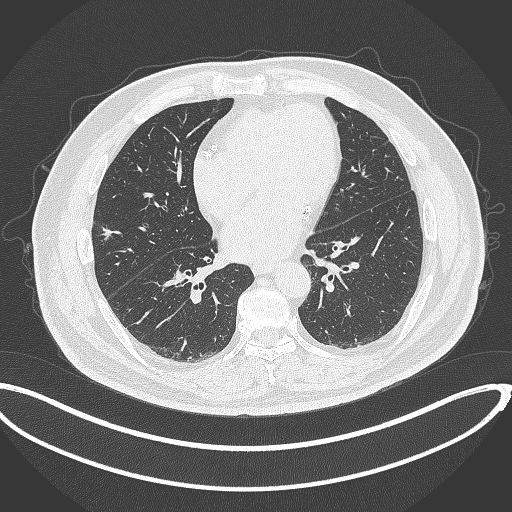
Chest CT, one axial slice; lung window (W 1500 / L -600 HU); 1 mm slice thickness; 512 × 512 image matrix, field of view 427 × 427 mm. Patient: male, 68 years. Case-level facts recorded for this patient, not image findings: clinical TNM (as recorded): T1c N0 M0; histopathological grade: G2.
Structures marked on this image (bounding box drawn by a radiologist):
- lung tumour (recorded histology: adenocarcinoma): bounding box [x1, y1, x2, y2] px = [102, 225, 114, 243]